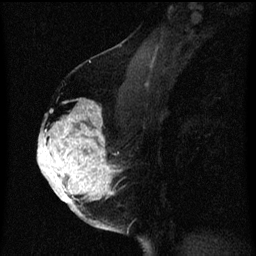
Breast MRI (dynamic contrast-enhanced), one sagittal slice. Position 37 of 60 along the scan axis. Dynamic contrast-enhanced series, image 2 of 3 at this slice position (ordered by acquisition). 1.5 T. TE 4.2 ms, TR 8 ms. 2 mm slice thickness. 256 × 256 image matrix. Patient: female, 56 years.
Outlined on this slice (semi-automatic segmentation, software-assisted and operator-edited):
- analysis volume of interest (the breast-tissue region the enhancement analysis was run in; not a lesion): bounding box (x1, y1, x2, y2) in pixels: (40, 100, 121, 217)
- tumour enhancement mask (voxels above the 70 % enhancement threshold inside the analysis volume of interest): (40, 102, 121, 217)